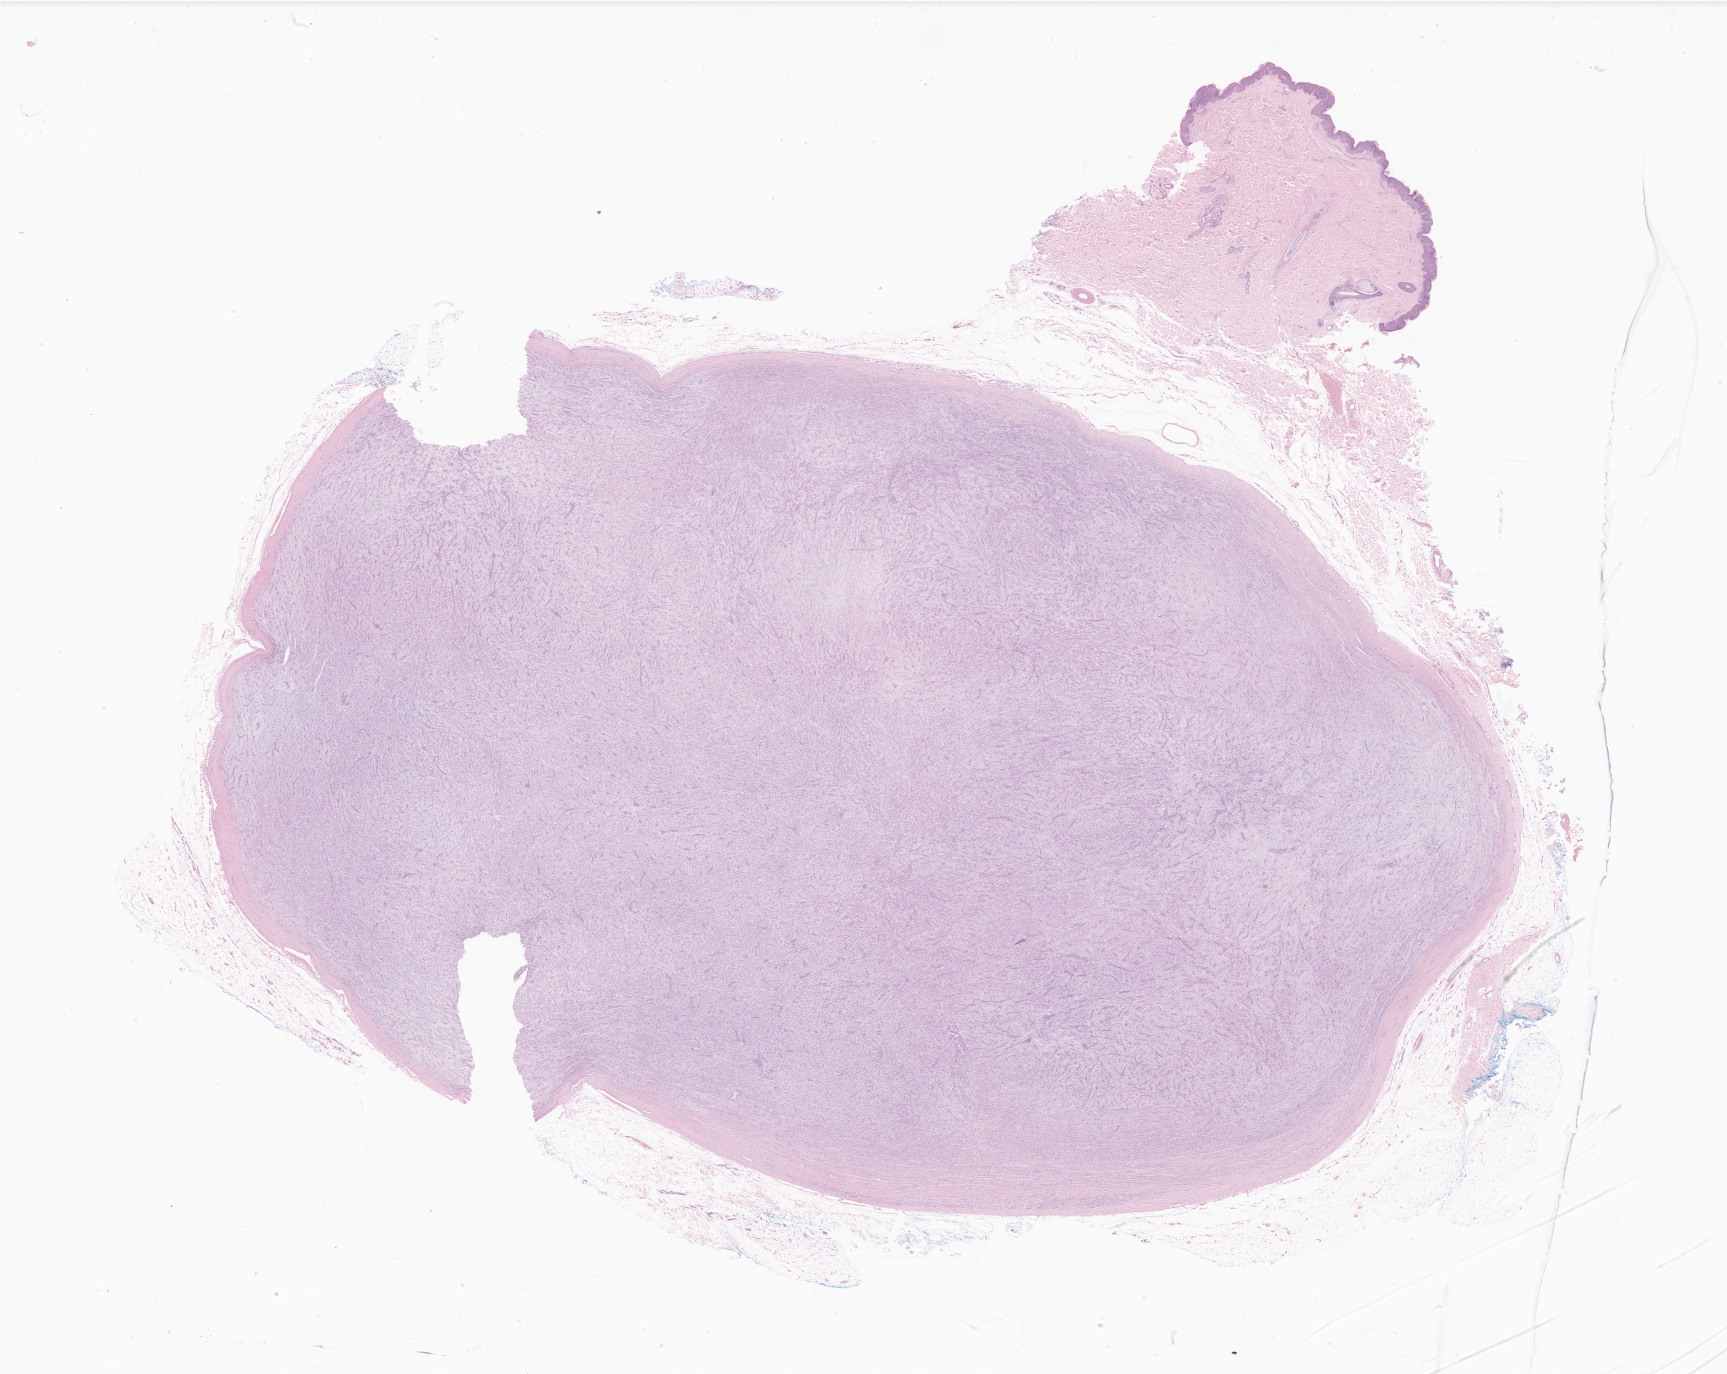
Haematoxylin and eosin whole-slide image of tumor tissue from the skin of lower limb, low-resolution overview of the scanned area, about 29.1 x 23.2 mm, FFPE section. Patient male; age 188 months (15 years 8 months).
- recorded diagnosis: Myxofibrosarcoma